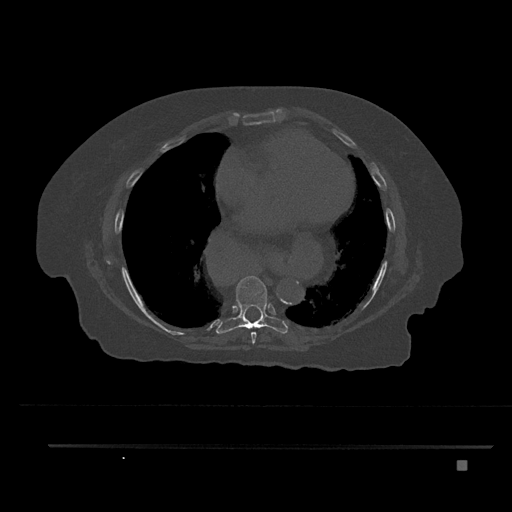
CT including the spine, one axial slice. Position 451 of 797 along the scan axis. Reconstruction kernel Br40s/3. Bone window (W 1800 / L 400 HU). 0.5 mm slice thickness. 512 × 512 image matrix, field of view 437 × 437 mm. Patient: female, 76 years. From the clinical record (not read from this slice): primary cancer: lung; vertebrae with lytic lesions (as recorded): T11, L3.
Annotated regions visible in this slice (semi-automatically segmented with operator editing):
- T7 vertebra: box from (x=251, y=332) to (x=257, y=344) px
- T8 vertebra: (x=216, y=276)–(x=288, y=334)